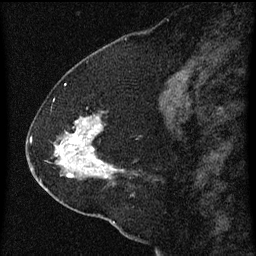
Breast MRI (dynamic contrast-enhanced), one sagittal slice. Slice 25 of 60 in the series (ordered by position). Dynamic contrast-enhanced series, image 2 of 3 at this slice position (ordered by acquisition). 1.5 T. TE 4.2 ms, TR 8 ms. 256 × 256 image matrix, field of view 180 × 180 mm. Female patient, age 47 years.
Outlined on this slice (semi-automatic segmentation, software-assisted and operator-edited):
- analysis volume of interest (the breast-tissue region the enhancement analysis was run in; not a lesion): bounding box (x1, y1, x2, y2) in pixels: (36, 98, 138, 213)
- tumour enhancement mask (voxels above the 70 % enhancement threshold inside the analysis volume of interest): (55, 118, 112, 179)